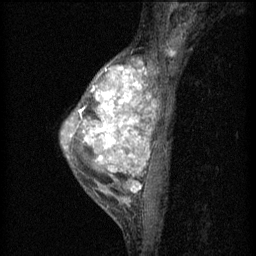
Breast MRI (dynamic contrast-enhanced), one sagittal slice. 3 images stored at this slice position (order not interpretable as contrast timing). 1.5 T. TE 4.2 ms, TR 11 ms. 256 × 256 image matrix. Female patient, age 40 years.
Annotated regions visible in this slice (semi-automatic segmentation, software-assisted and operator-edited):
- analysis volume of interest (the breast-tissue region the enhancement analysis was run in; not a lesion): bounding box (x1, y1, x2, y2) in pixels: (61, 50, 166, 203)
- tumour enhancement mask (voxels above the 70 % enhancement threshold inside the analysis volume of interest): (79, 64, 156, 193)